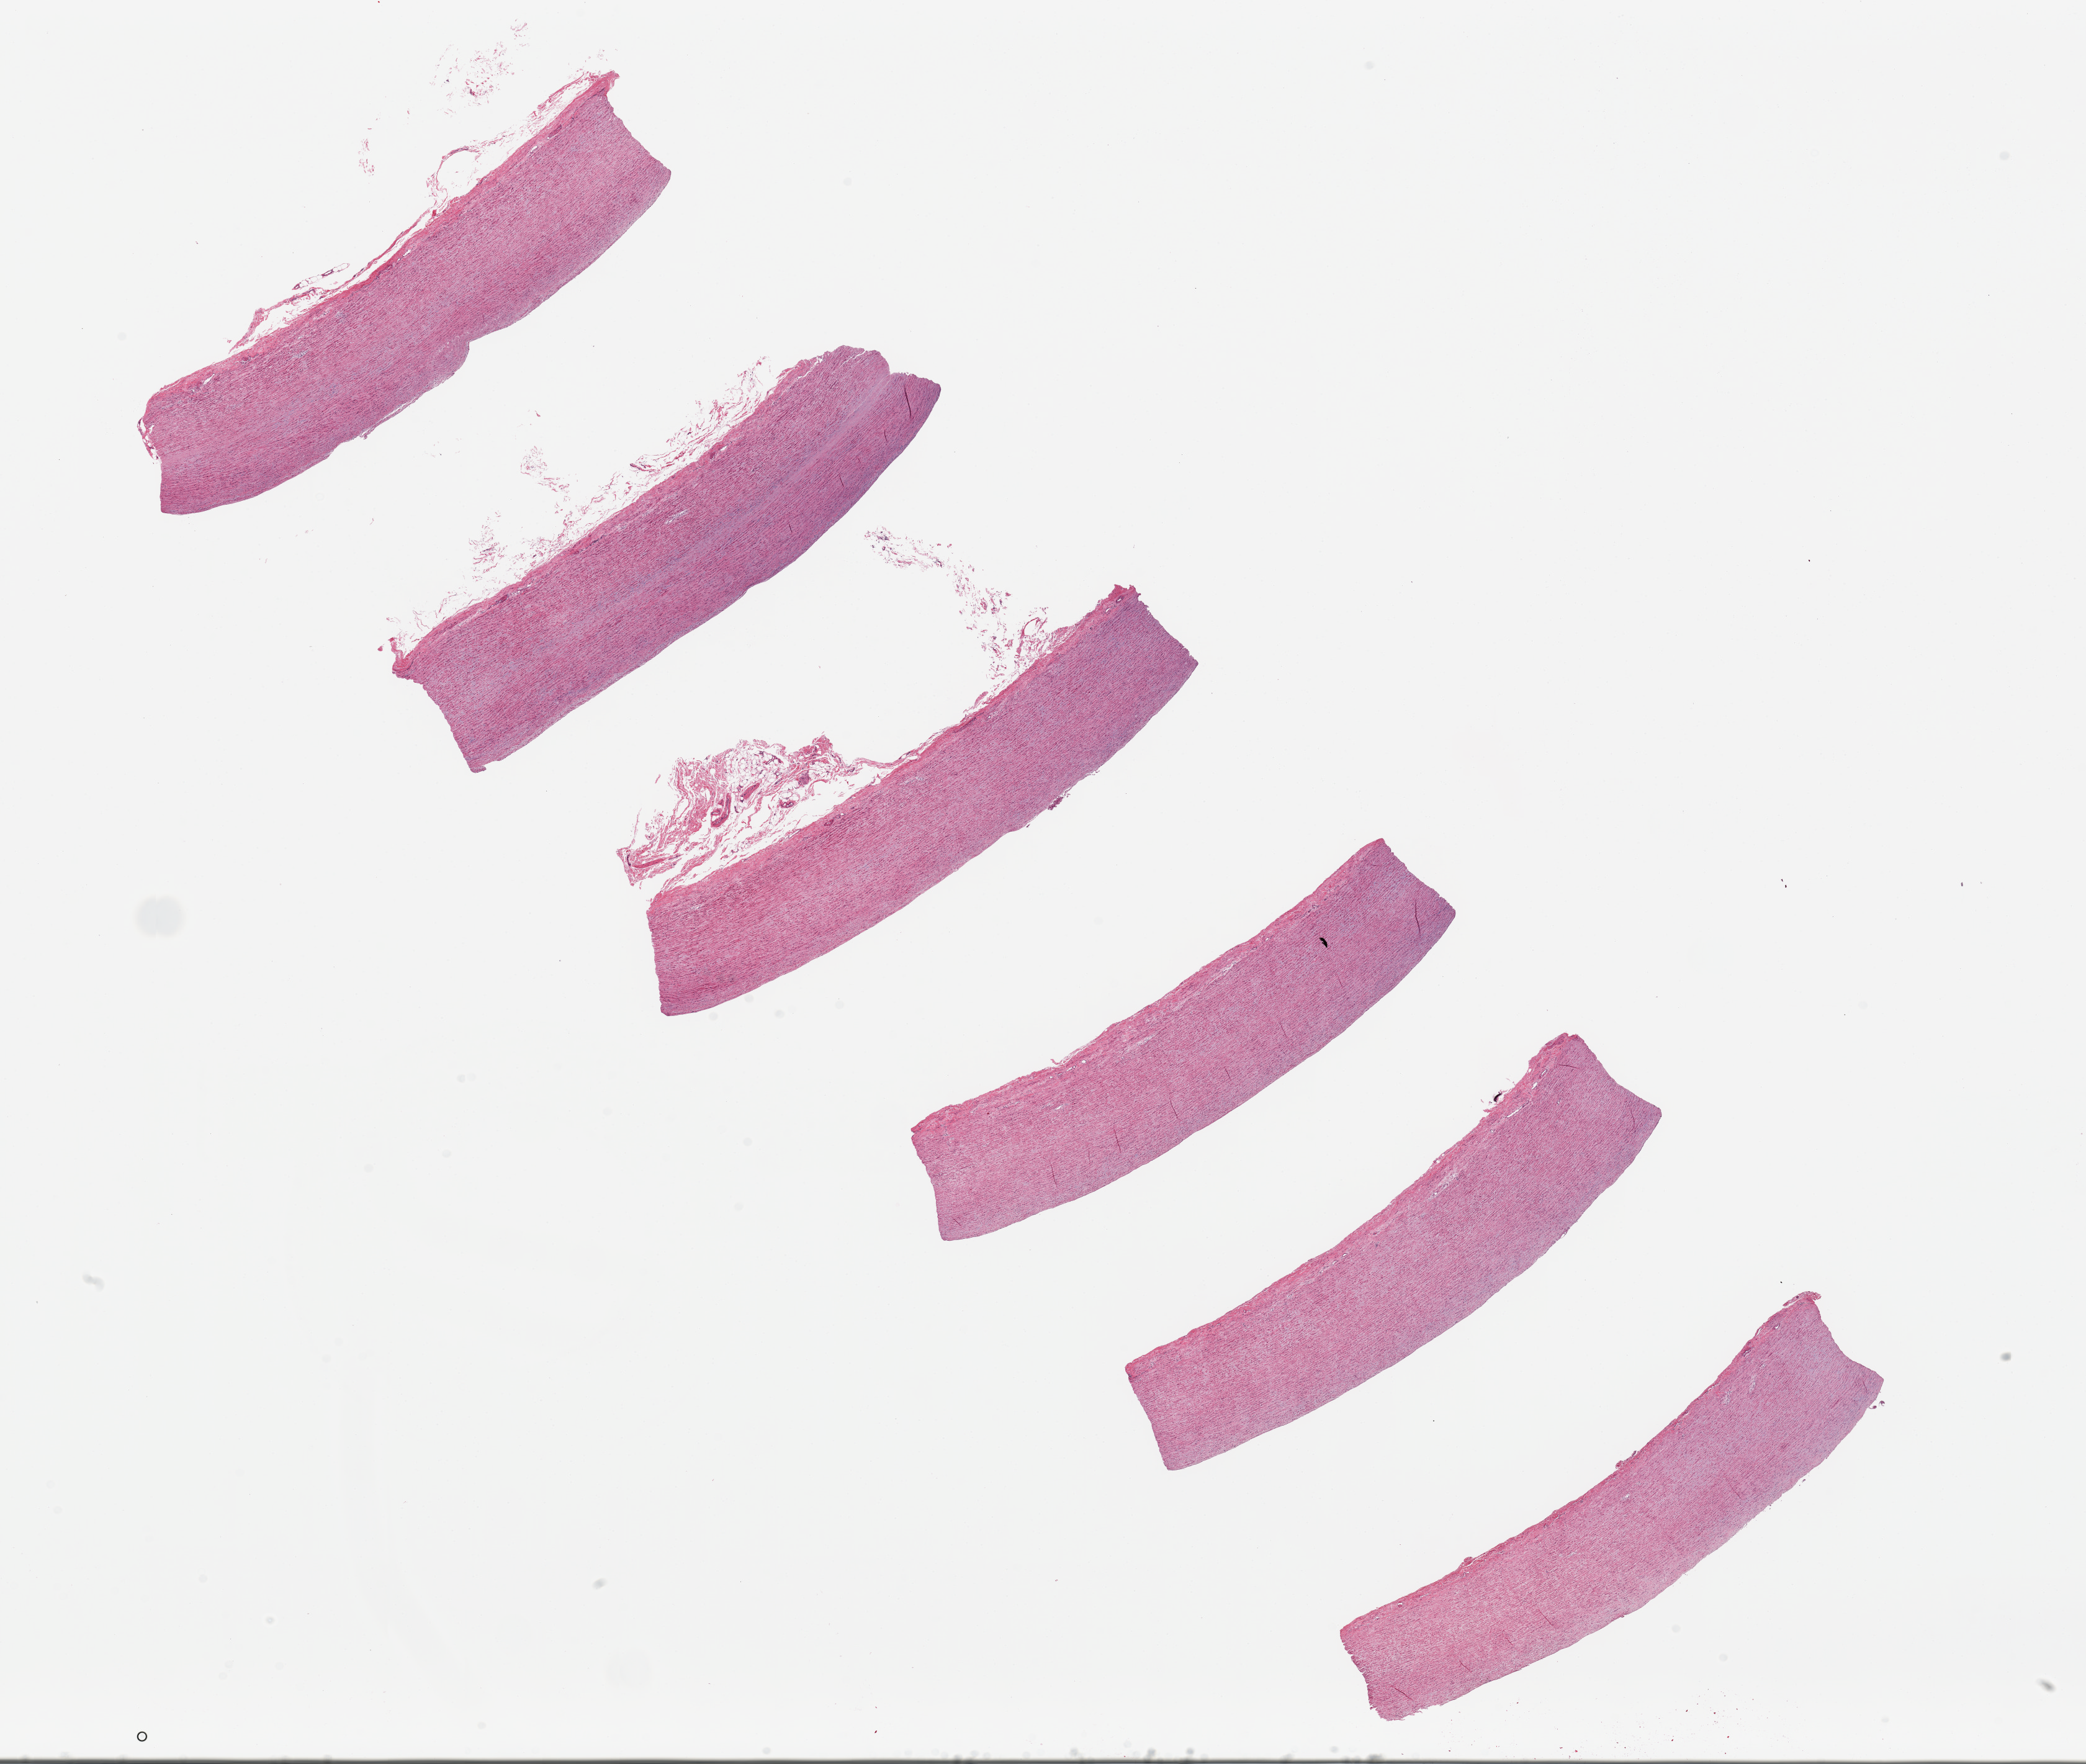
Whole-slide image, haematoxylin and eosin stain, brightfield — low-resolution overview of the scanned area, about 26.6 x 22.5 mm (from a 20x scan), PAXgene-fixed paraffin-embedded (PFPE) section, section of aorta (target tissue), donor tissue sample. Male donor.
* pathologist's review note for this sample: 6 ~7x1.5mm pieces